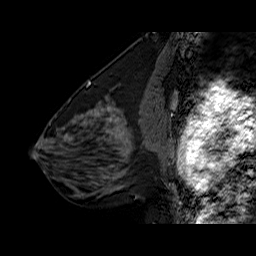
Breast MRI (dynamic contrast-enhanced), one sagittal slice; position 29 of 60 along the scan axis; dynamic contrast-enhanced series, time point 2 of 6 at this slice position (early post-contrast); 1.5 T; TE 6.3 ms, TR 32.5 ms; 256 × 256 image matrix, field of view 200 × 200 mm. Female patient. From the clinical record (not read from this slice): setting: breast cancer imaged before/during neoadjuvant chemotherapy; receptor status: triple-negative.
Outlined on this slice (semi-automatically segmented with operator editing):
- analysis volume of interest (the breast-tissue region the enhancement analysis was run in; not a lesion): bounding box [x1, y1, x2, y2] px = [108, 126, 154, 177]
- tumour enhancement mask (voxels above the 100 % enhancement threshold inside the analysis volume of interest): [111, 129, 125, 138]